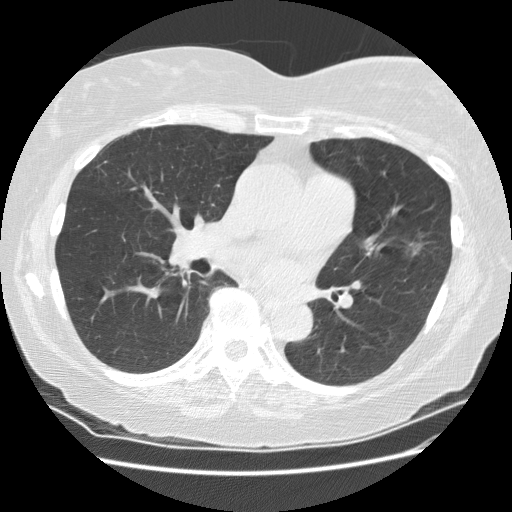
Low-dose screening chest CT, one axial slice; position 95 of 180 along the scan axis; 120 kVp; lung window (W 1500 / L -600 HU); 2.5 mm slice thickness; 512 × 512 image matrix.
Structures marked on this image (outlined manually by an expert reader):
- lesion 1 (tumor, upper lobe of left lung): bounding box <406,241,428,258> (left, top, right, bottom; pixels)